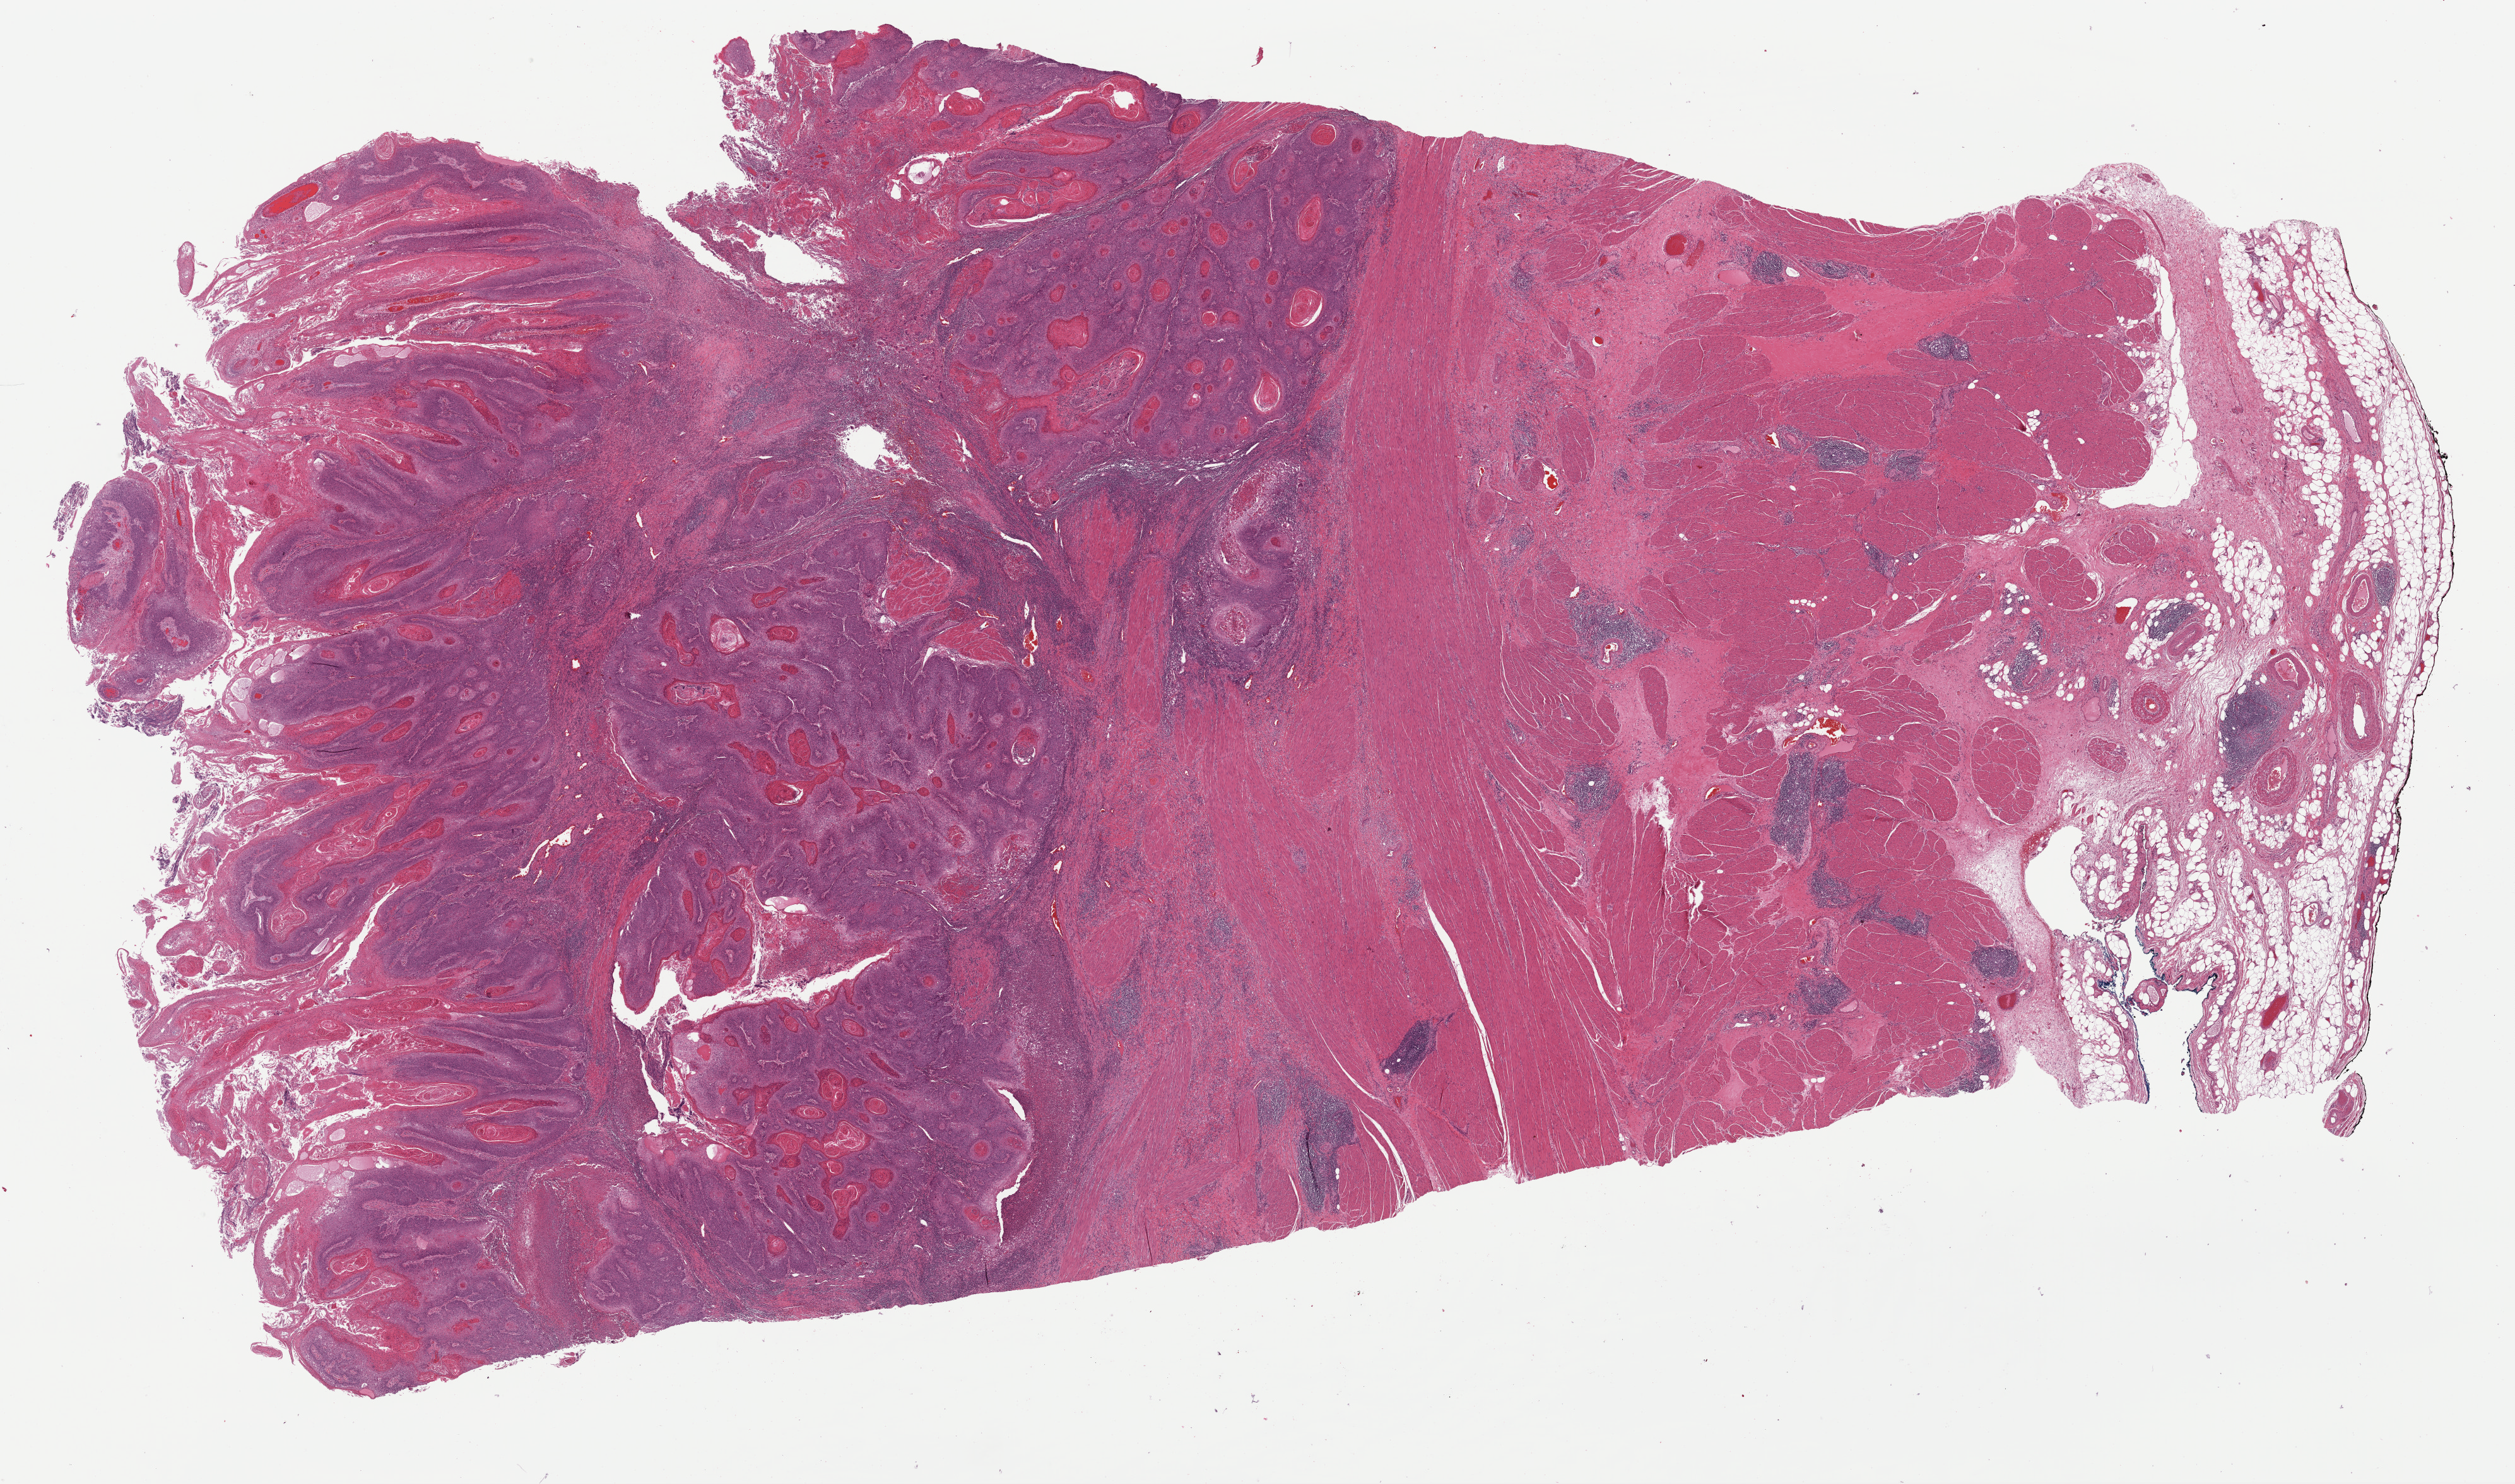
Digitized H&E tissue section (whole slide), a low-resolution overview of the entire scanned area, about 31.5 x 18.6 mm, formalin-fixed paraffin-embedded (FFPE) diagnostic section, bladder, primary tumour sample. Patient: female, age at initial diagnosis 43 years. Histologic grade: high grade.
Histologic diagnosis: Transitional cell carcinoma (anterior wall of bladder). AJCC pathologic stage: II (7th edition). Lymph nodes positive (case pathology): 0 of 58 examined.